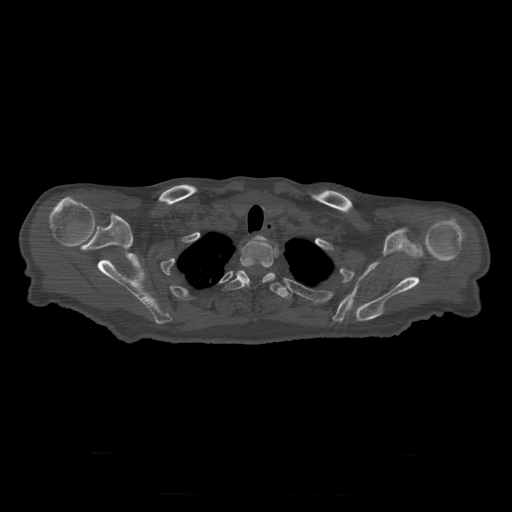
CT including the spine, one axial slice. Position 267 of 397 along the scan axis. Reconstruction kernel STANDARD. 120 kVp. Bone window (W 1800 / L 400 HU). 1.25 mm slice thickness. 512 × 512 image matrix, field of view 510 × 510 mm. Patient age 73 years. Case-level facts recorded for this patient, not image findings: primary cancer: prostate.
Annotated regions visible in this slice (semi-automatically segmented with operator editing):
- T1 vertebra: box from (x=254, y=236) to (x=265, y=240) px
- T2 vertebra: (x=240, y=240)–(x=276, y=283)
- T3 vertebra: (x=223, y=271)–(x=292, y=298)